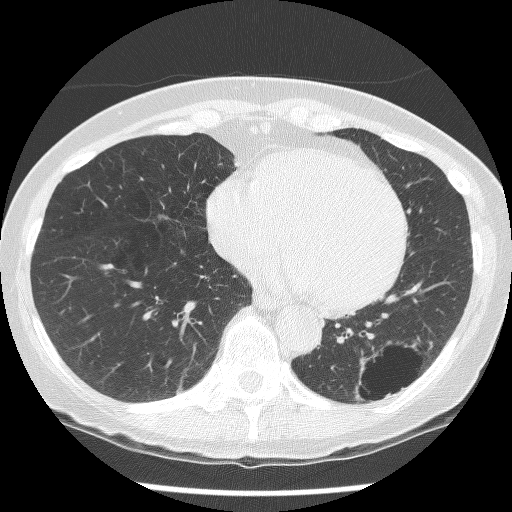
Chest CT (low-dose screening protocol), one axial image. Second screening round (one year after baseline). Lung window (W 1500 / L -600 HU). Lung (sharp) reconstruction kernel (BONE). 120 kVp. 512 × 512 image matrix, field of view 300 × 300 mm. Female, age 61 years at enrolment. Current smoker at enrolment.
Expert reader's lesion annotation, box from (x=333, y=329) to (x=436, y=417) px. The screening reader recorded 2 non-calcified nodules or masses ≥4 mm on this exam (left lower lobe, left lower lobe); which of them this box marks is not recorded. Lung cancer was diagnosed 585 days after this screen (after the third annual screen): non-small cell carcinoma, left lower lobe, poorly differentiated (G3), stage IB (AJCC 6th edition), 100 mm at pathology.